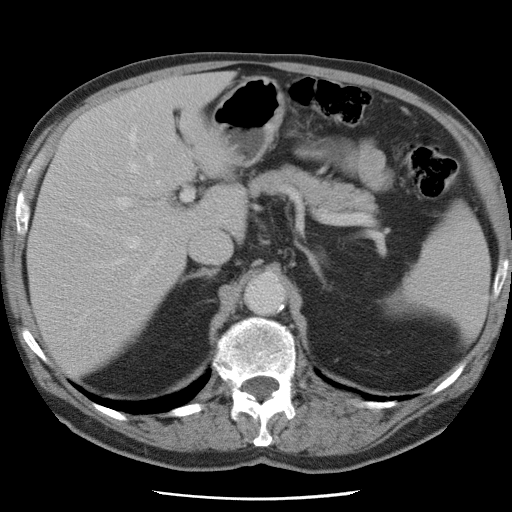
Contrast-enhanced abdominal CT, one axial slice; position 48 of 78 along the scan axis; intravenous contrast given; soft-tissue window (W 400 / L 40 HU); 512 × 512 image matrix. Male patient, age 75 years. Case-level facts recorded for this patient, not image findings: diagnosis: colorectal cancer liver metastases, imaged before liver resection; multiple liver metastases: yes; largest metastasis: 2.4 cm; disease in both lobes: yes.
Annotated regions visible in this slice (outlined manually by an expert reader):
- hepatic veins: box from (x=59, y=131) to (x=160, y=268) px
- liver: (x=29, y=74)–(x=247, y=376)
- planned liver remnant (the part of the liver to remain after resection): (x=29, y=123)–(x=195, y=376)
- portal vein (with intrahepatic branches): (x=116, y=138)–(x=193, y=279)